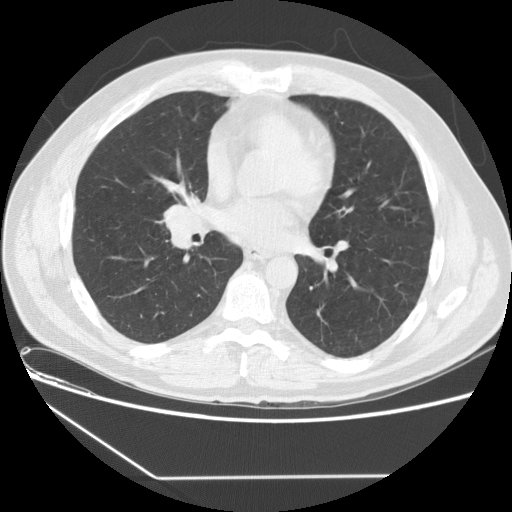
Low-dose screening chest CT, one axial slice; position 71 of 154 along the scan axis; reconstruction kernel STANDARD; lung window (W 1500 / L -600 HU); 512 × 512 image matrix, field of view 370 × 370 mm.
Annotated regions visible in this slice (expert manual segmentation):
- lesion 1 (tumor, middle lobe of right lung): bounding box <165,204,199,233> (left, top, right, bottom; pixels)